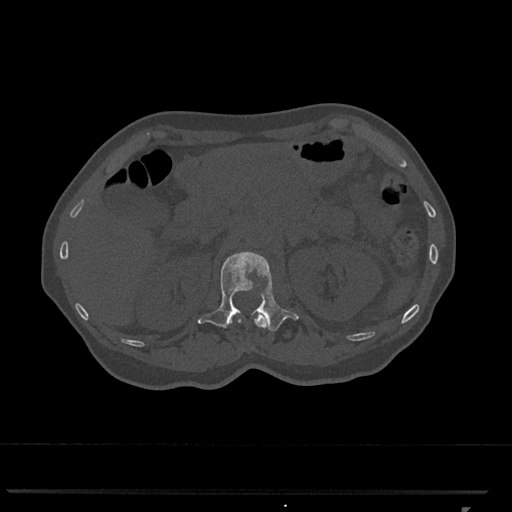
CT including the spine, one axial slice; position 416 of 793 along the scan axis; bone window (W 1800 / L 400 HU); 0.5 mm slice thickness; 512 × 512 image matrix, field of view 380 × 380 mm. Female patient, age 62 years. From the clinical record (not read from this slice): primary cancer: renal.
Structures marked on this image (semi-automatically segmented with operator editing):
- L1 vertebra: bounding box (x1, y1, x2, y2) in pixels: (198, 252, 299, 331)
- T12 vertebra: (230, 314, 267, 328)